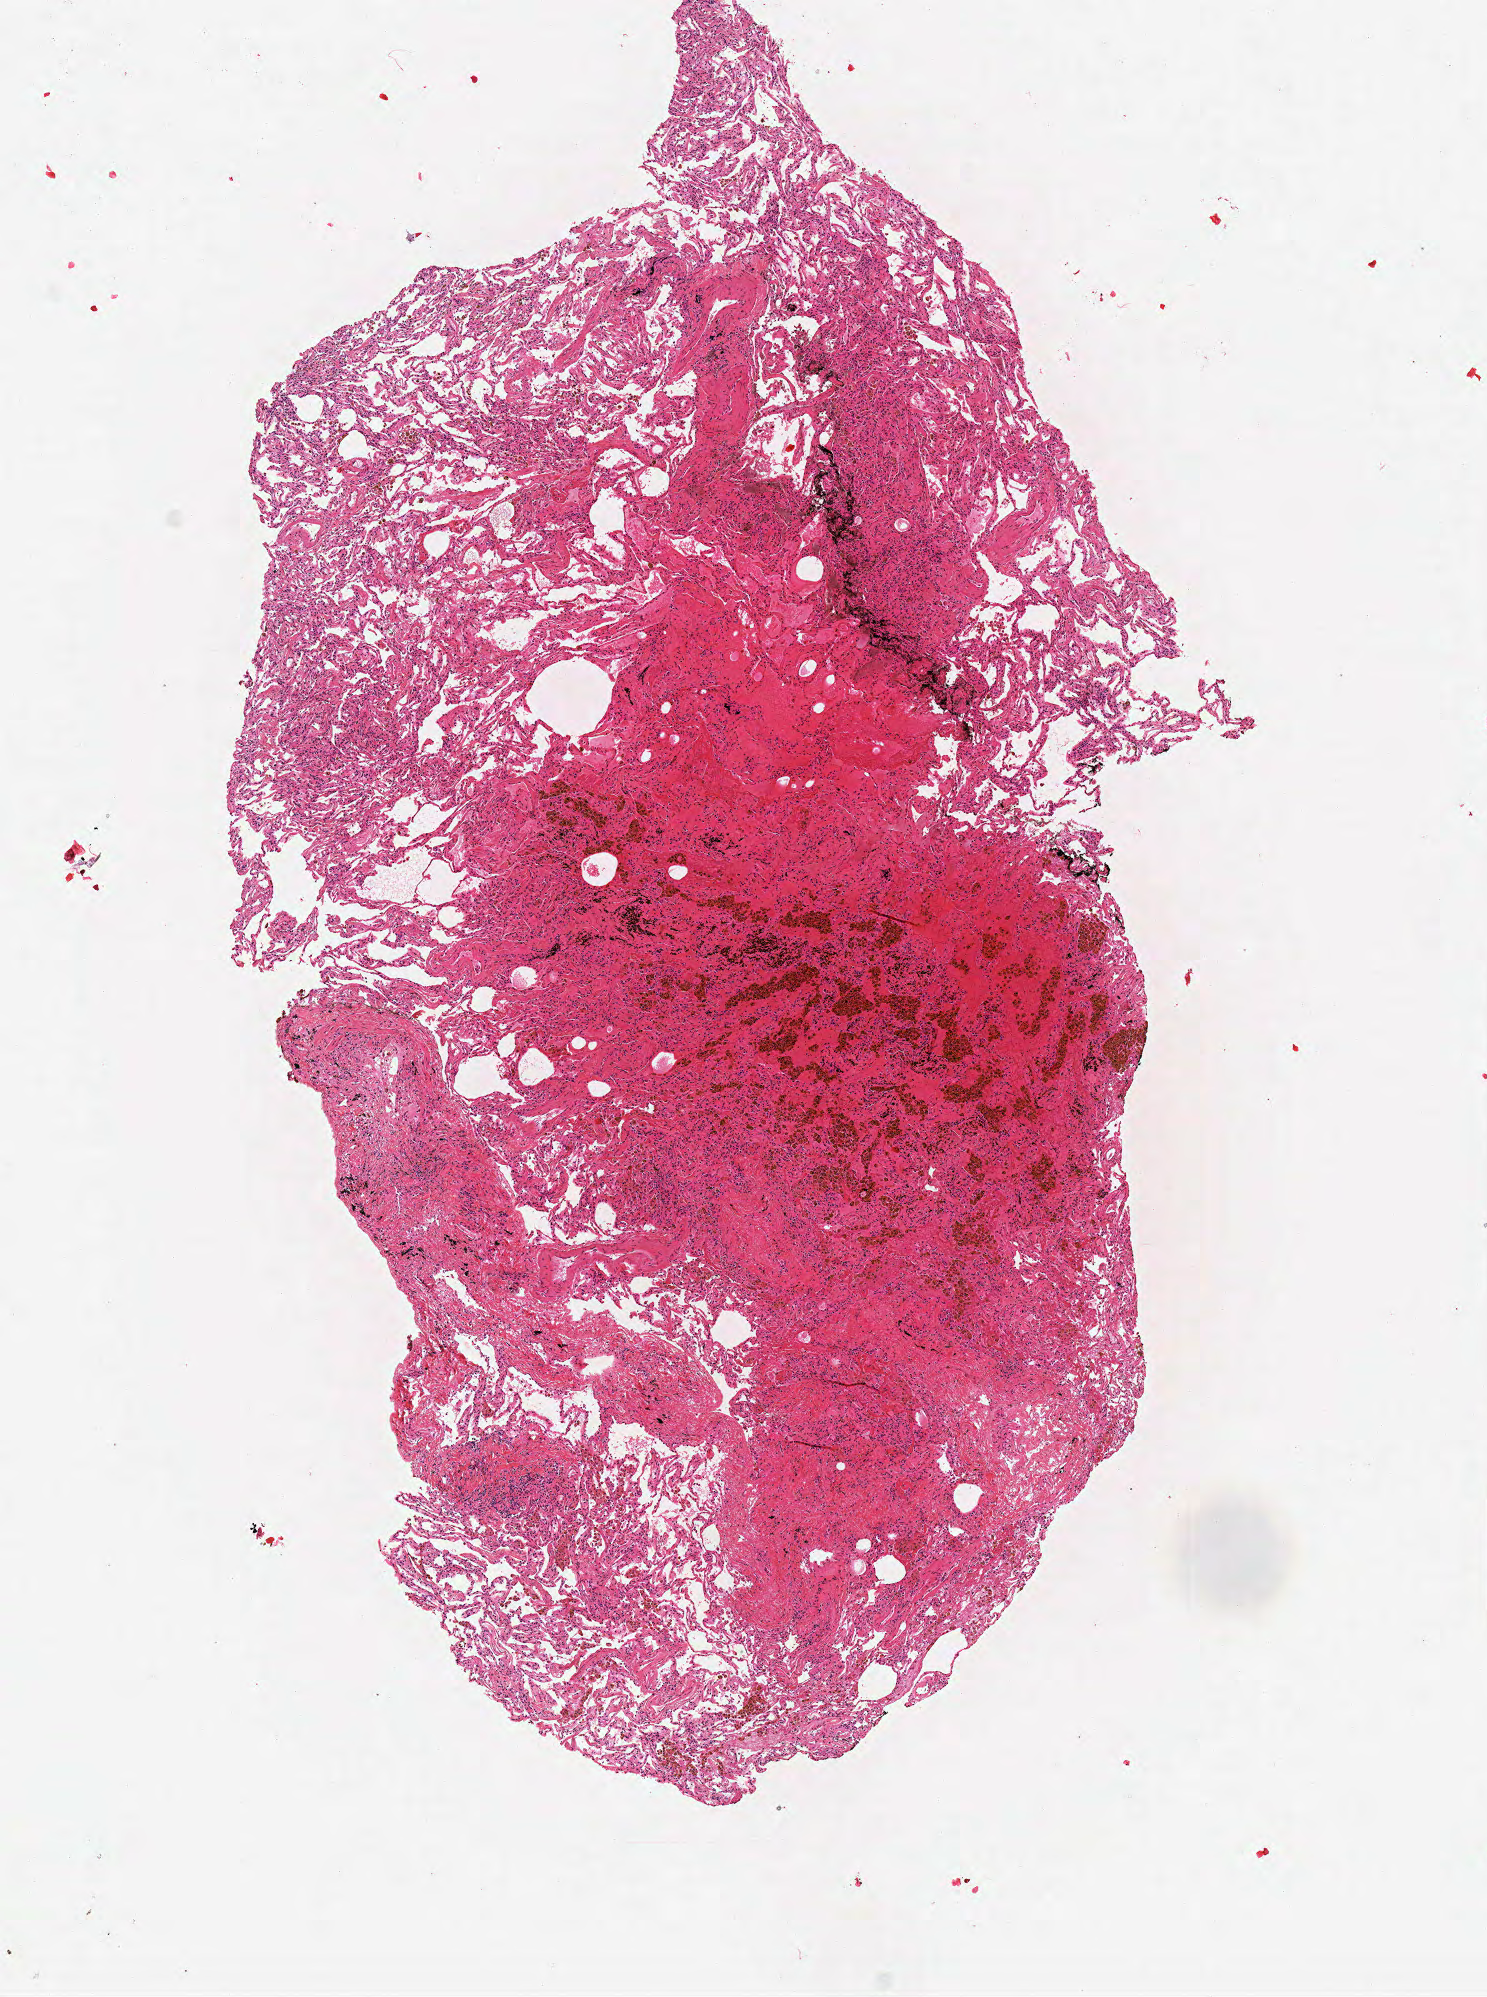
H&E whole-slide image — low-resolution overview of the scanned area, about 5.9 x 7.9 mm (acquisition: 40x scan), frozen section from the top of the tissue portion, lung, solid tissue normal (non-tumour tissue) sample. Male, age 69 years at initial diagnosis.
This section: solid tissue normal (non-tumour) sample from the same patient. Patient diagnosis: Squamous cell carcinoma, NOS.